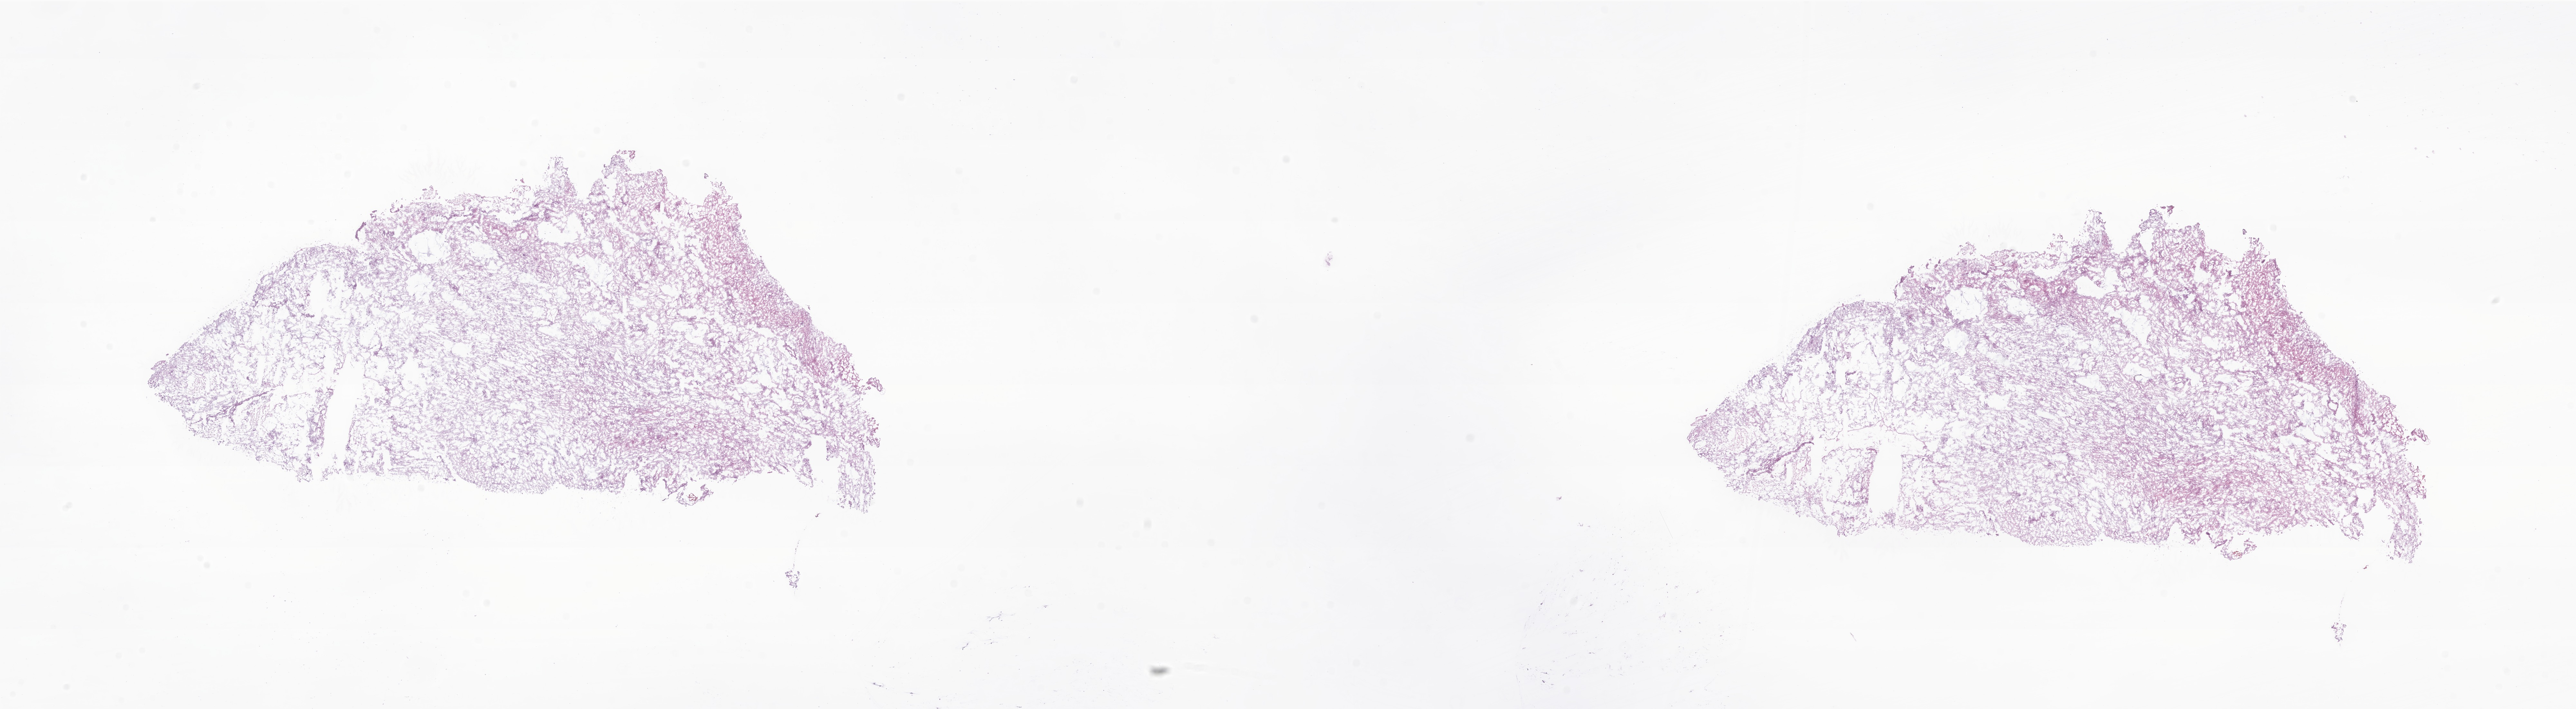
H&E whole-slide image of tumor tissue from the brain — a low-resolution overview of the entire scanned area, about 33.7 x 9.3 mm. Frozen section (OCT-embedded). Female patient, age 69 months.
Diagnosis (ICD-O-3 morphology term): Neoplasm, uncertain whether benign or malignant.